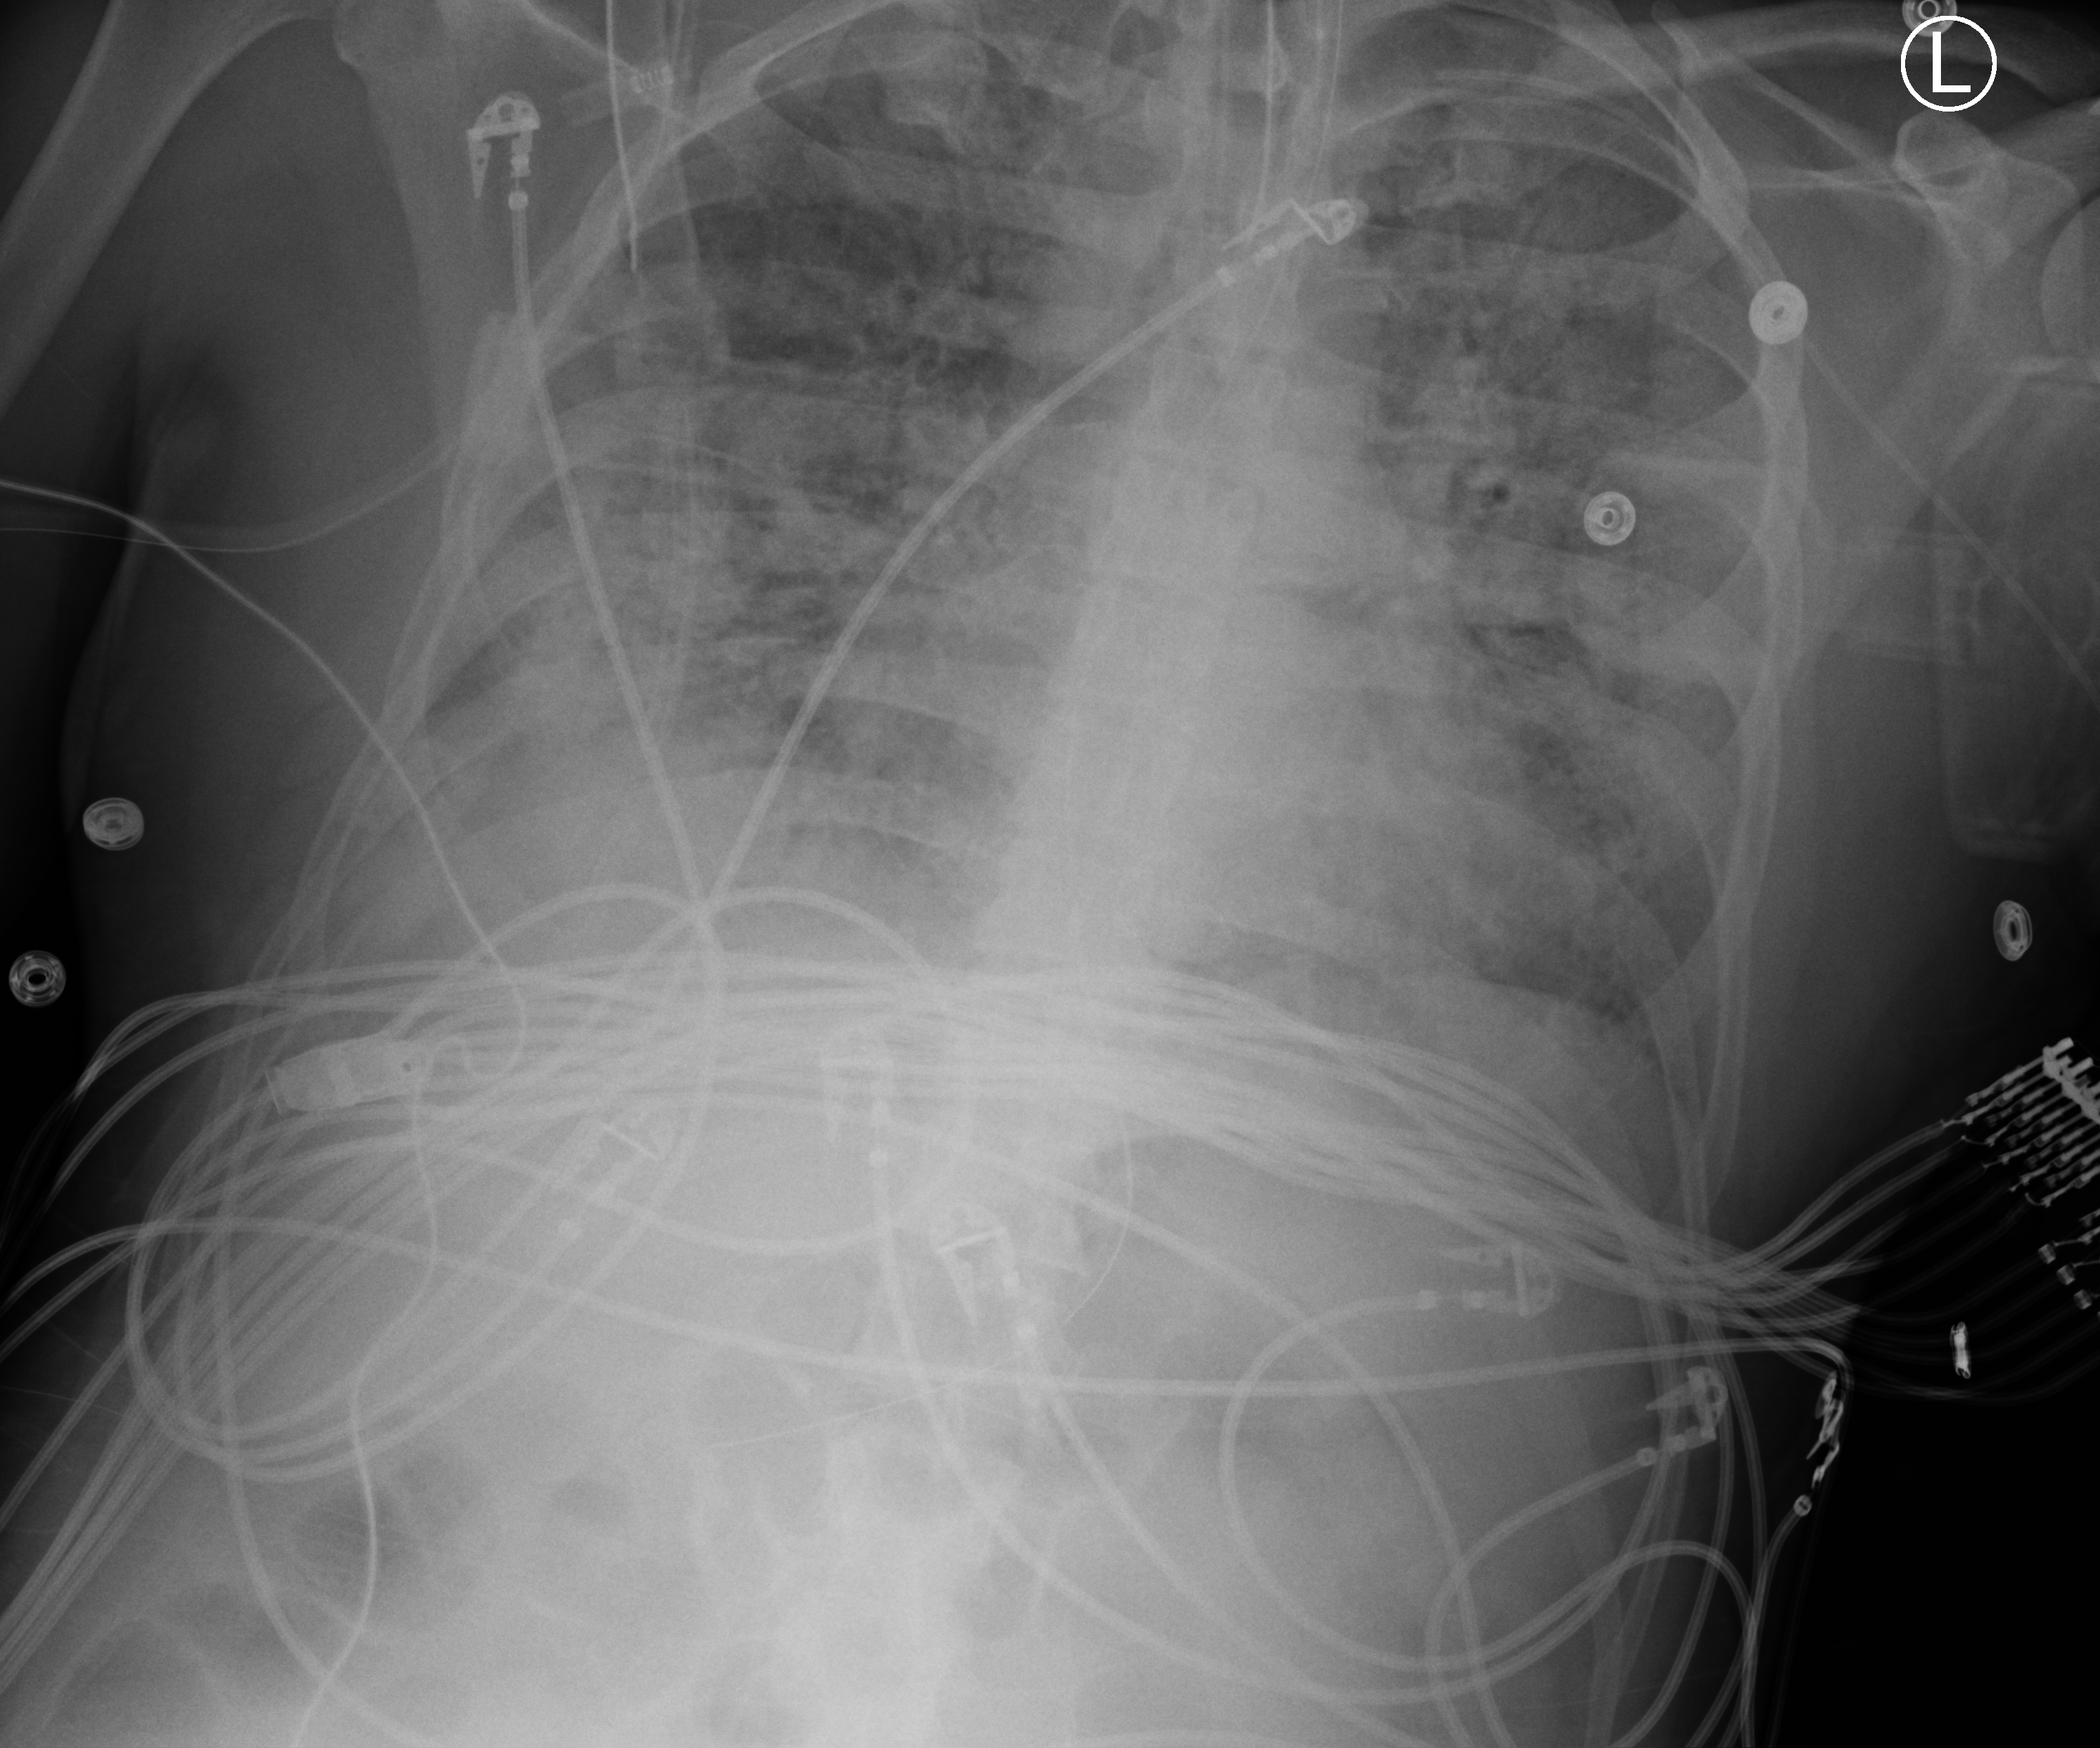
Portable chest radiograph; anteroposterior (AP) projection. Male patient hospitalised with COVID-19, age 18–59 years.
Admission-level facts for this patient (not findings on this image; timing relative to this image not recorded): chronic kidney disease (admission record): no; COPD (admission record): no; mechanically ventilated during this hospital stay: yes.